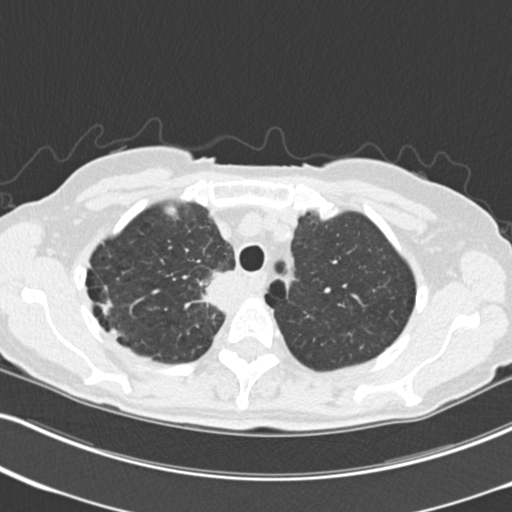
Low-dose screening chest CT, one axial slice; slice 180 of 226 in the series (ordered by position); lung window (W 1500 / L -600 HU); 2 mm slice thickness; 512 × 512 image matrix, field of view 322 × 322 mm.
Annotated regions visible in this slice (outlined manually by an expert reader):
- lesion 1 (tumor, mediastinum): box from (x=202, y=271) to (x=234, y=315) px